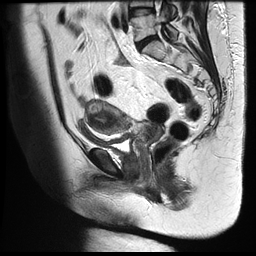
Pelvic MRI for cervical cancer, one sagittal slice. Position 19 of 35 along the scan axis. T2-weighted. 1.5 T. TE 122.8 ms, TR 4992 ms. 4 mm slice thickness. 256 × 256 image matrix, field of view 300 × 300 mm. Female patient, age 42 years.
Structures marked on this image (expert manual segmentation):
- uterus and cervix: bounding box [x1, y1, x2, y2] px = [84, 100, 163, 145]